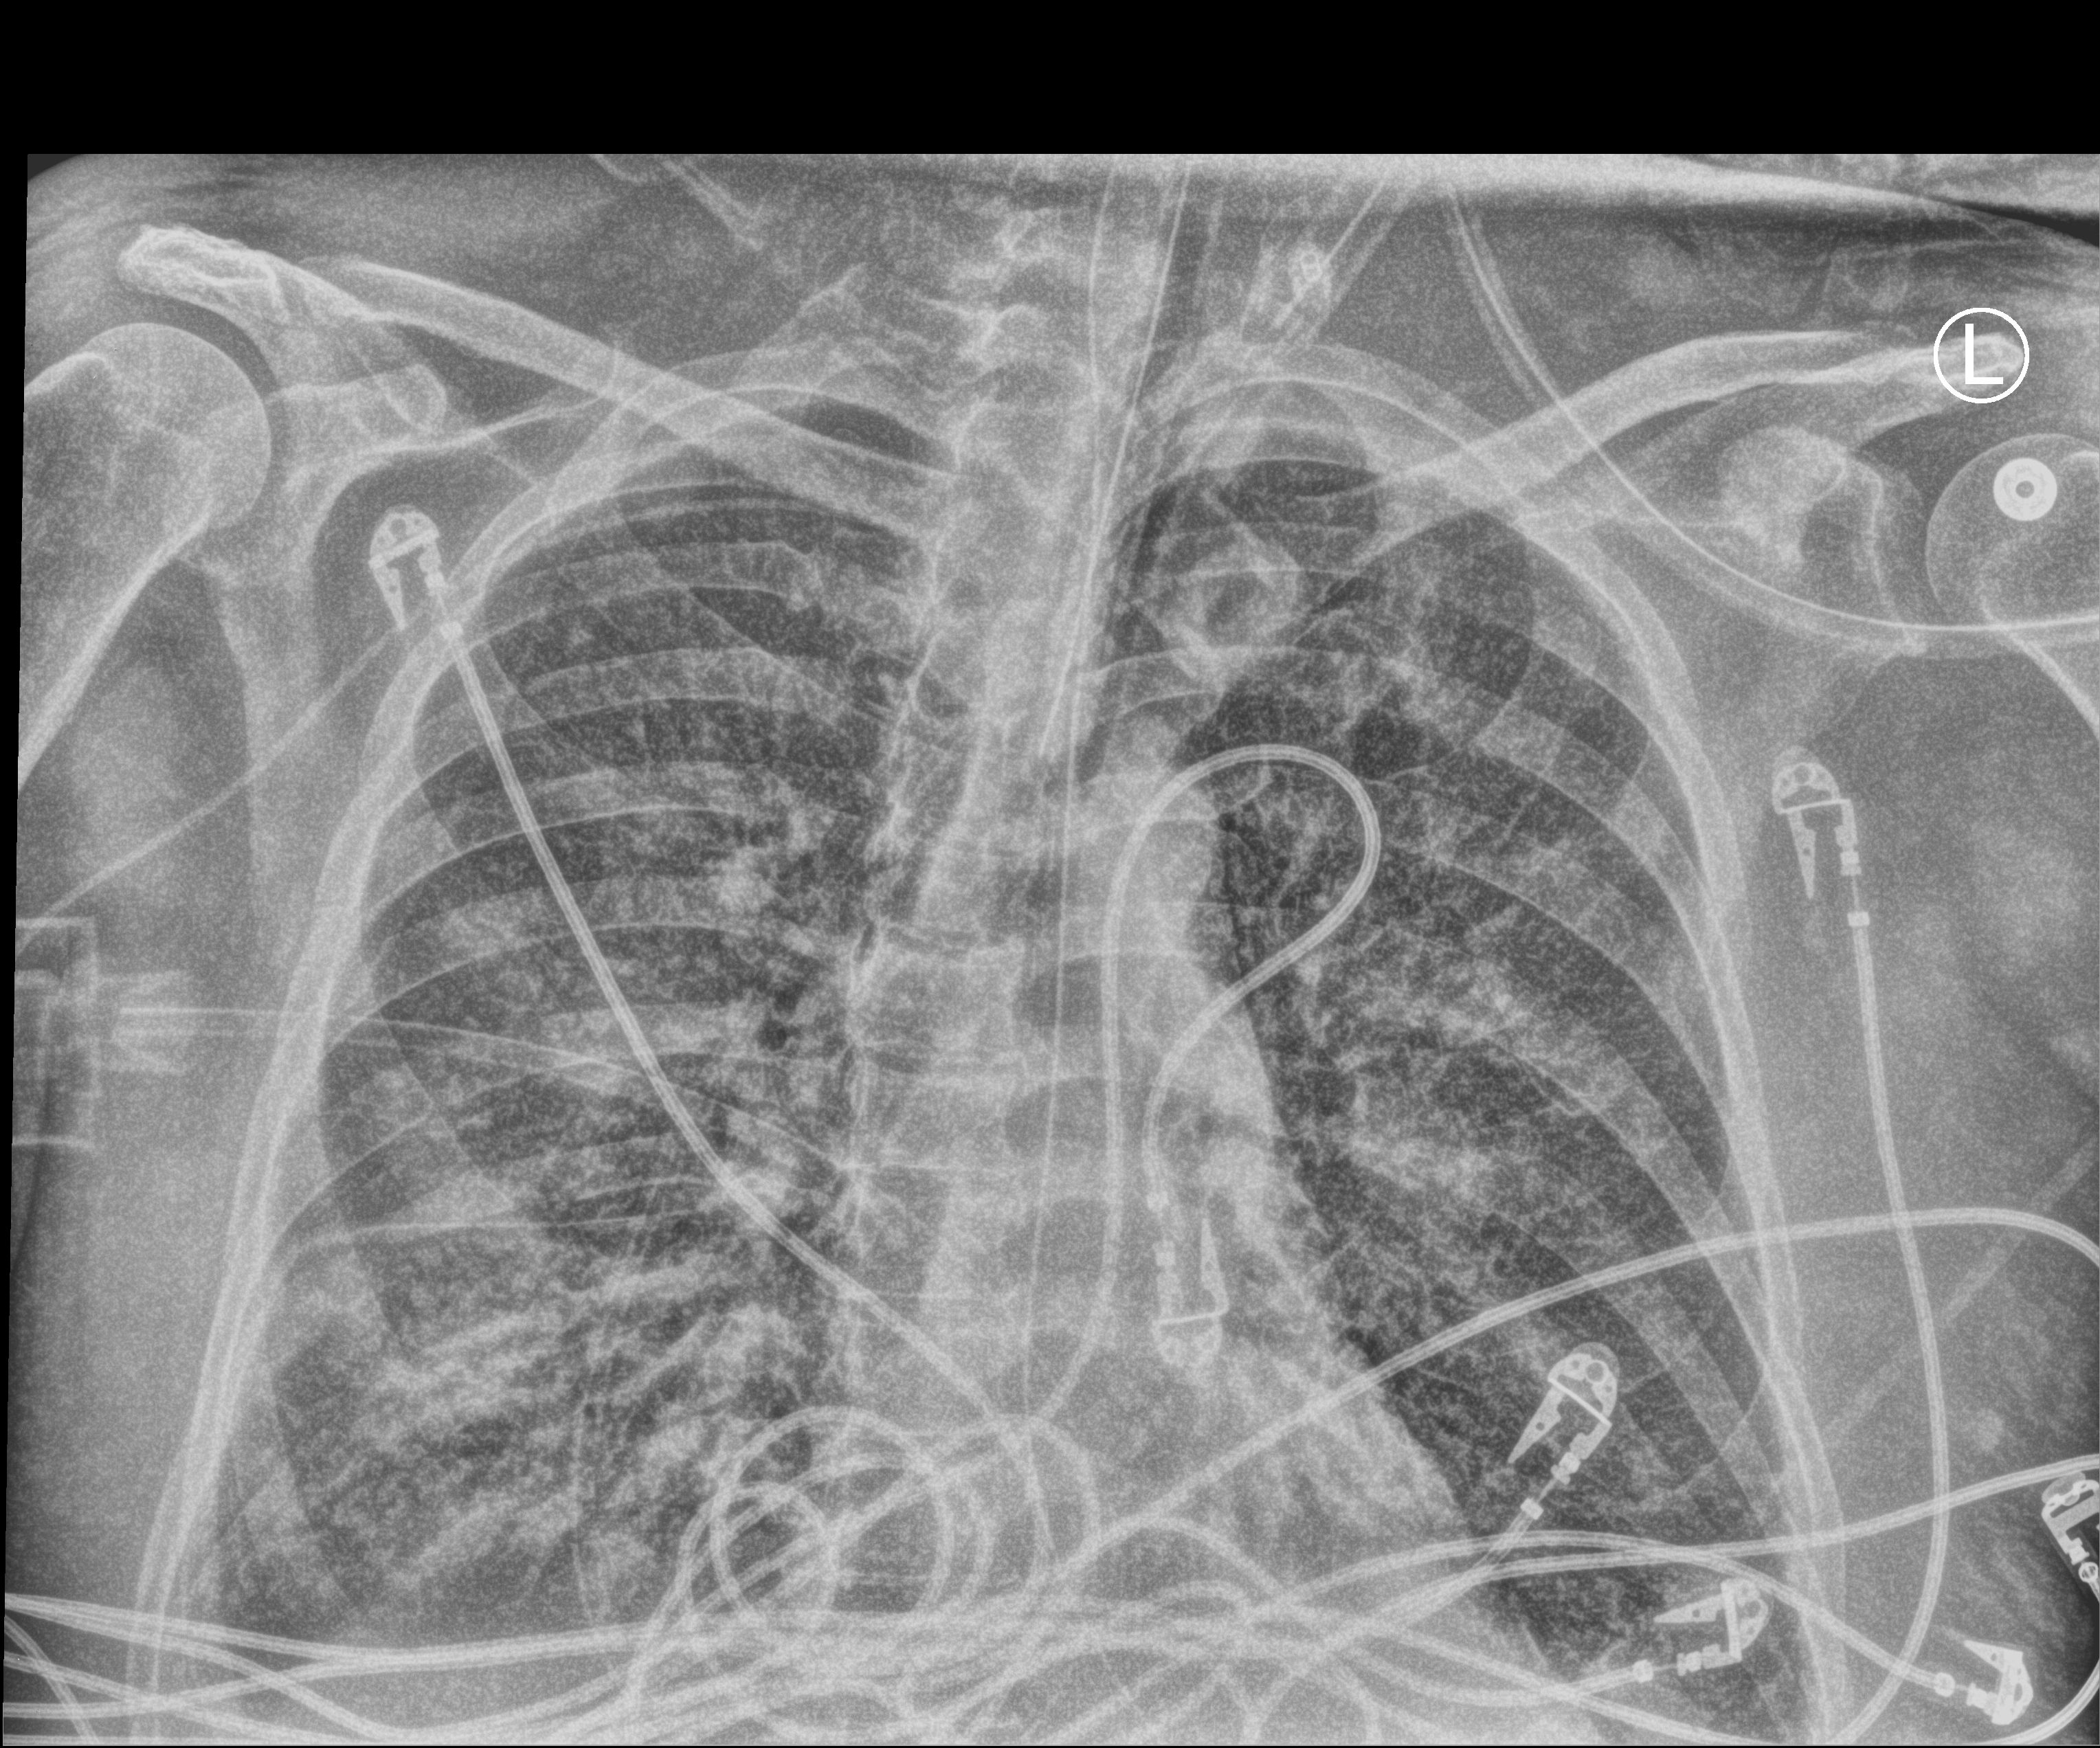
Chest X-ray (portable), anteroposterior (AP) projection. Patient hospitalised with COVID-19; male, aged 60–74 years.
From the hospital-stay record, not from the radiograph (when in the stay this image was taken is not recorded):
- length of hospital stay: 24 days
- admitted to intensive care during this hospital stay: yes